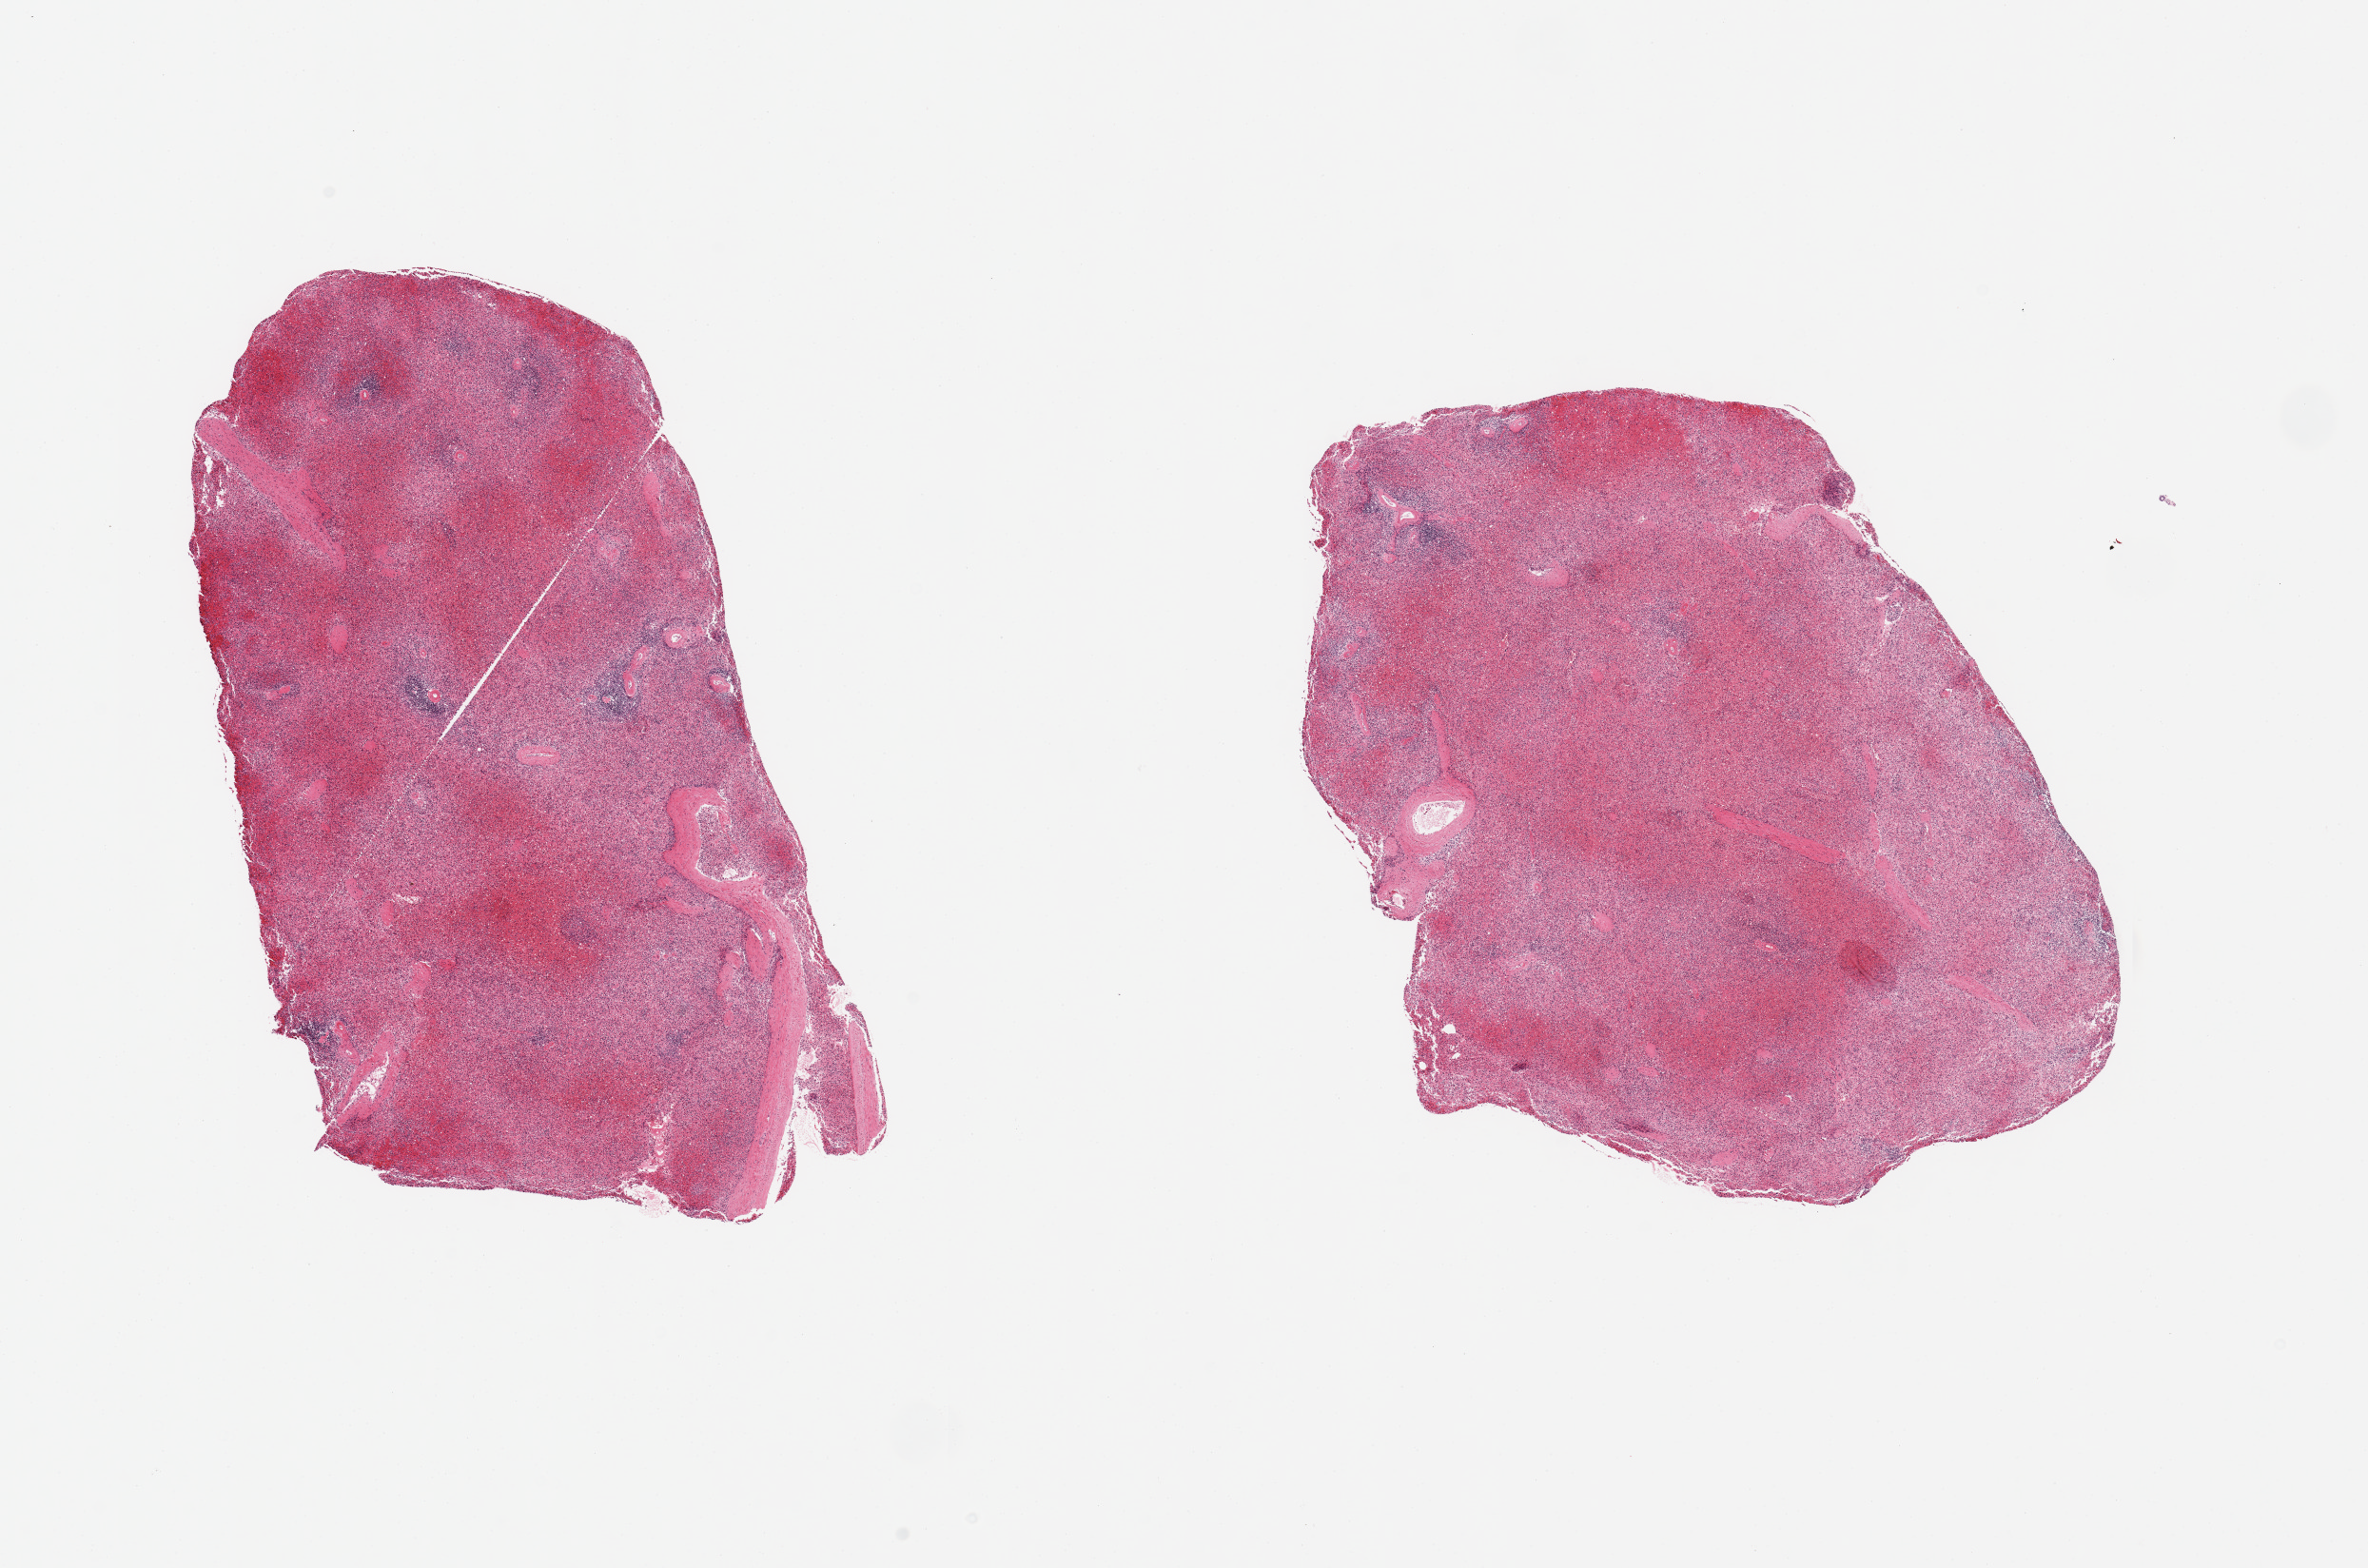
Haematoxylin and eosin whole-slide image — low-resolution overview of the scanned area, about 19.7 x 13.0 mm. PAXgene-fixed, paraffin-embedded tissue. Sampled site (target tissue): spleen. Donor tissue sample.
* reviewer comment on this tissue sample: 2 pieces, moderate congestion, advance autolysis